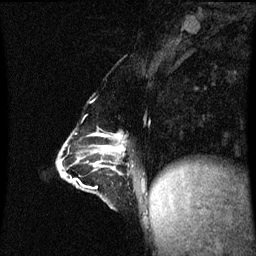
Breast MRI (dynamic contrast-enhanced), one sagittal slice. Dynamic contrast-enhanced series, image 2 of 3 at this slice position (ordered by acquisition). 1.5 T. TE 4.2 ms, TR 8.9 ms. 2 mm slice thickness. 256 × 256 image matrix. Patient: female, 47 years. Case-level facts recorded for this patient, not image findings: setting: breast cancer imaged before/during neoadjuvant chemotherapy; receptor status: HR-positive, HER2-negative.
Structures marked on this image (semi-automatically segmented with operator editing):
- analysis volume of interest (the breast-tissue region the enhancement analysis was run in; not a lesion): bounding box [x1, y1, x2, y2] px = [59, 130, 146, 209]
- tumour enhancement mask (voxels above the 70 % enhancement threshold inside the analysis volume of interest): [100, 134, 125, 153]